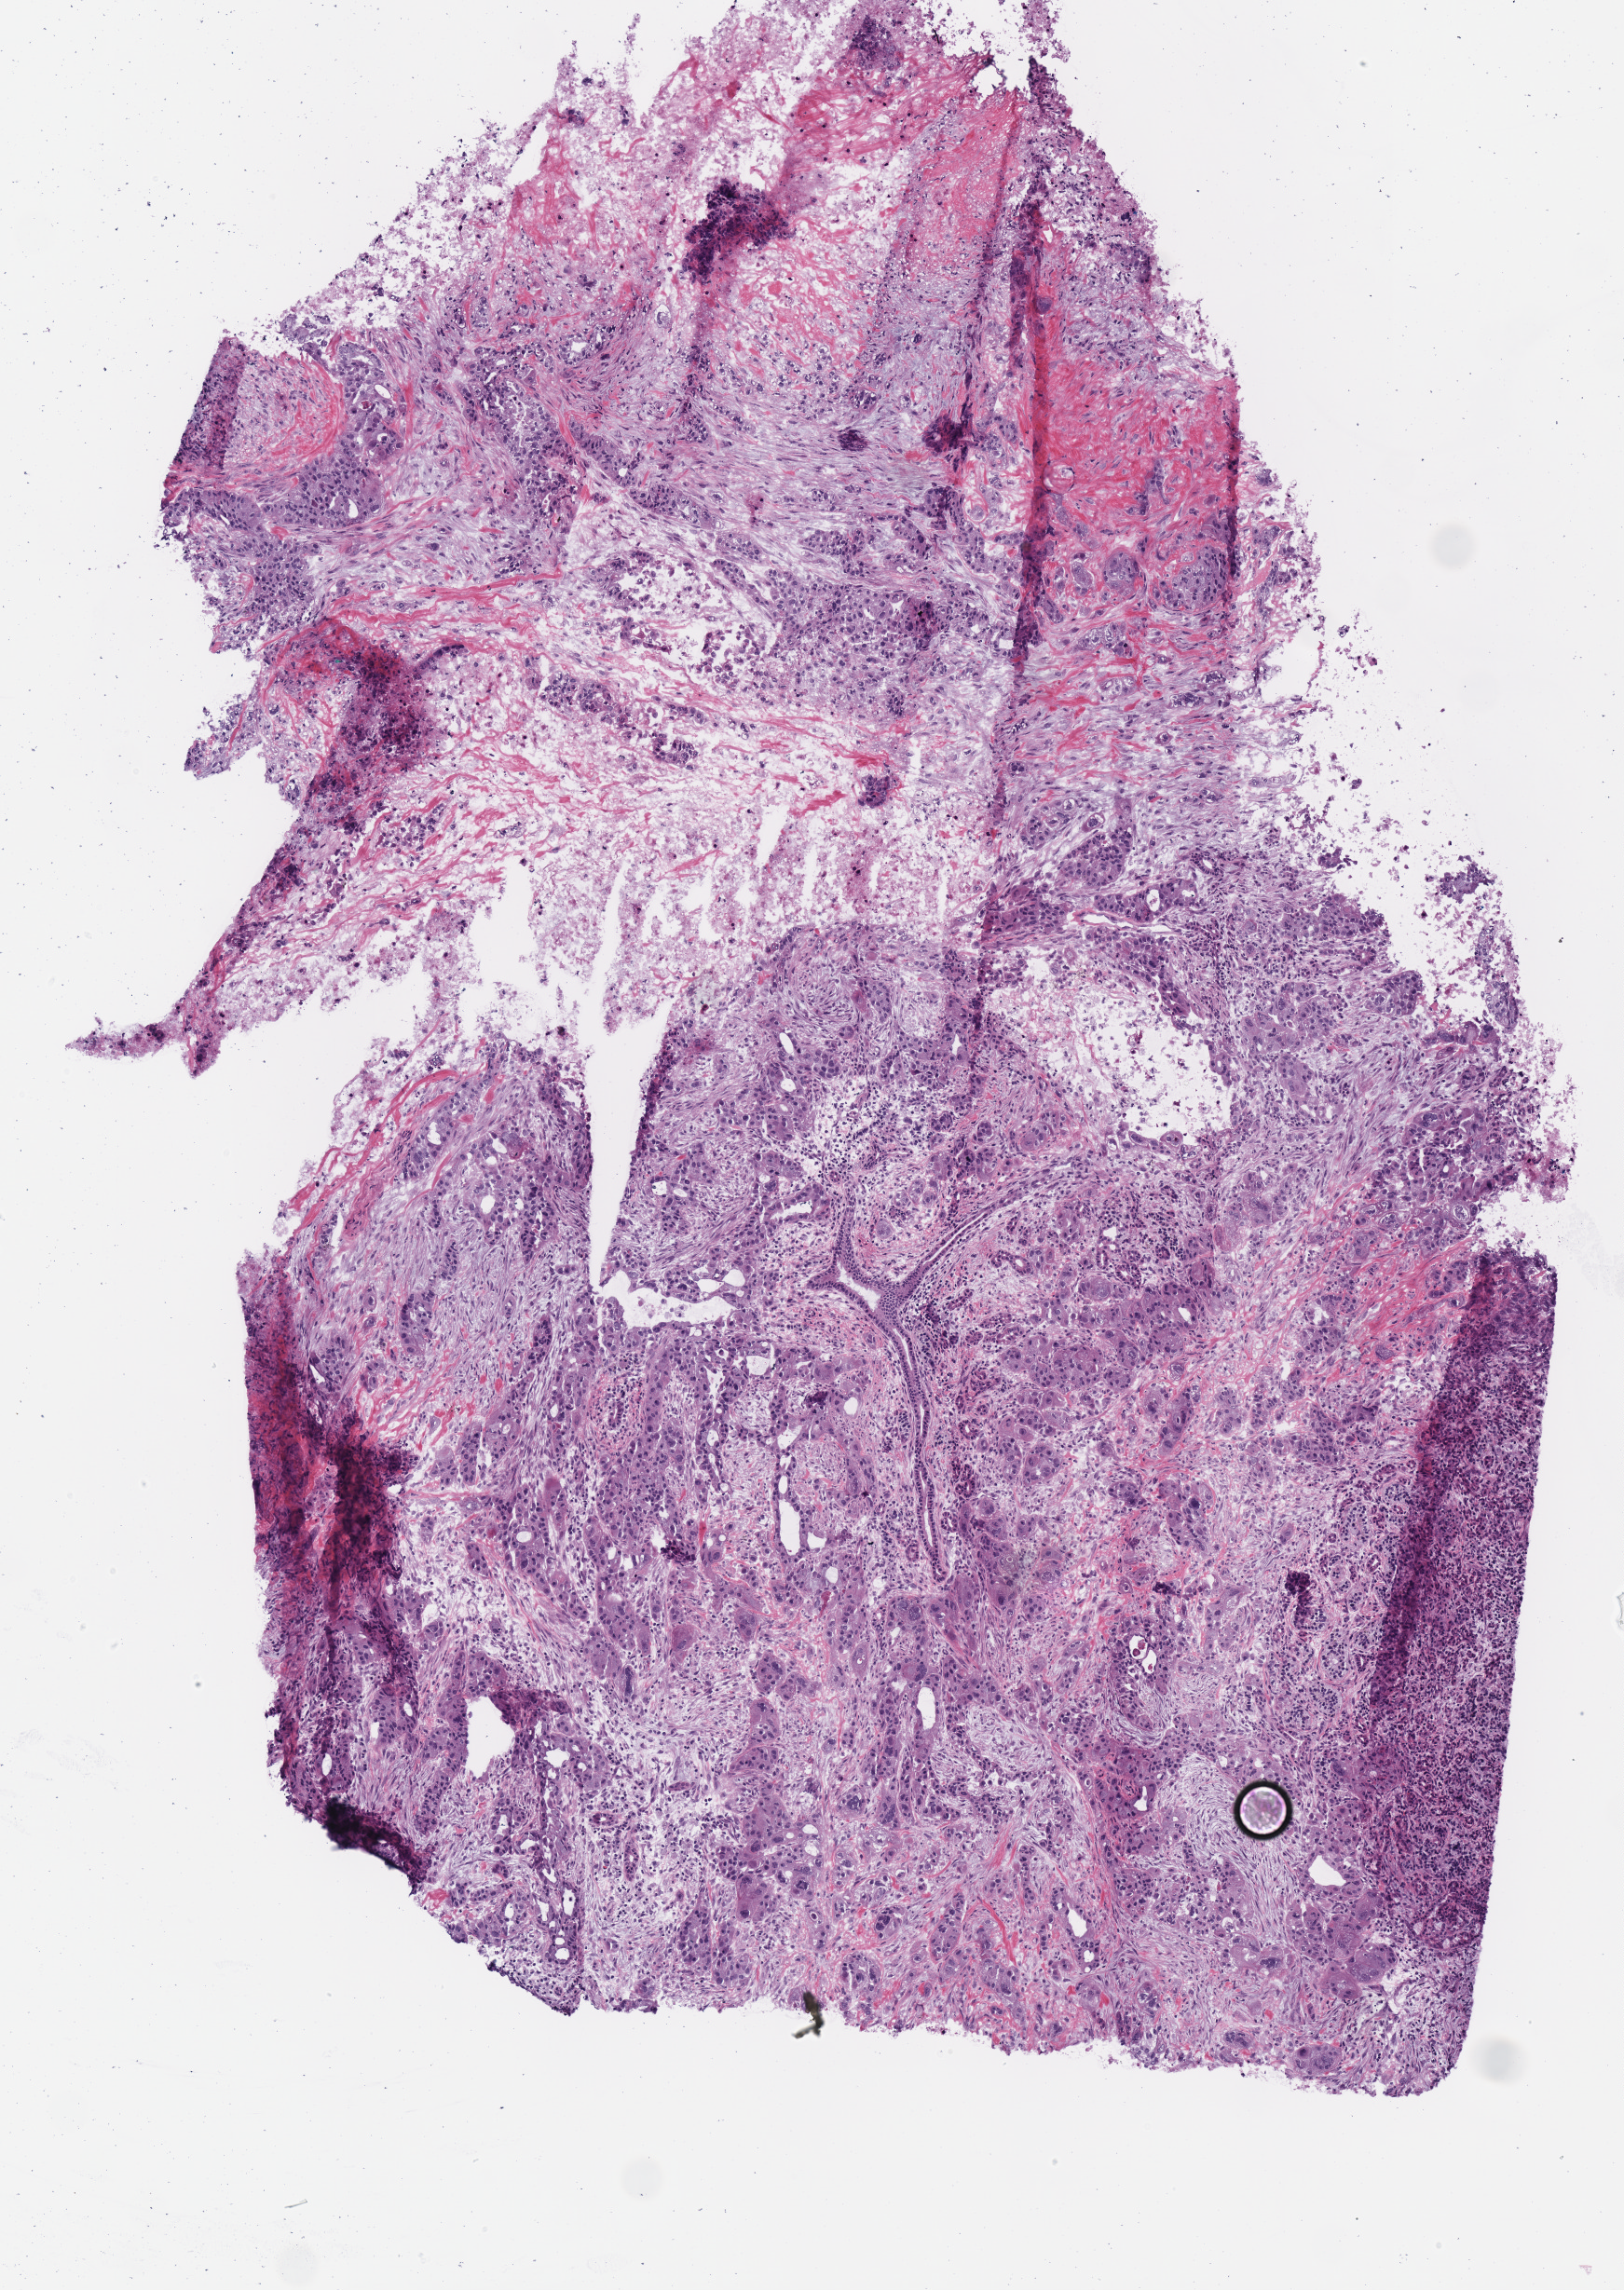
H&E-stained whole-slide image — whole scanned area (about 3.4 x 4.8 mm, acquisition: 40x scan) shown as a low-resolution overview. Frozen section from the top of the tissue portion. Pancreas, primary tumour sample. Patient: female, age at initial diagnosis 56 years. Histologic grade: G3 (poorly differentiated). Composition of this section per pathologist review: tumour cells 95%, tumour nuclei 70%, normal cells 2%, stromal cells 3%, necrosis 0%. Infiltration values recorded for this section: lymphocyte infiltration 10%, monocyte infiltration 5%, neutrophil infiltration 0%.
AJCC pathologic stage: IIB (7th edition). Histologic diagnosis: Adenocarcinoma, NOS (head of pancreas).